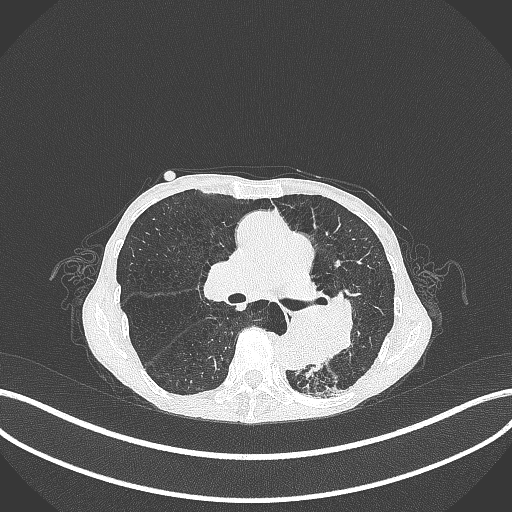
Chest CT, one axial slice; 120 kVp; lung window (W 1500 / L -600 HU); 1 mm slice thickness; 512 × 512 image matrix, field of view 400 × 400 mm. Patient: female, 70 years. Case-level facts recorded for this patient, not image findings: clinical TNM (as recorded): T3 N0 M0.
Outlined on this slice (bounding box drawn by a radiologist):
- lung tumour (recorded histology: small cell carcinoma): bounding box [x1, y1, x2, y2] px = [282, 295, 361, 365]